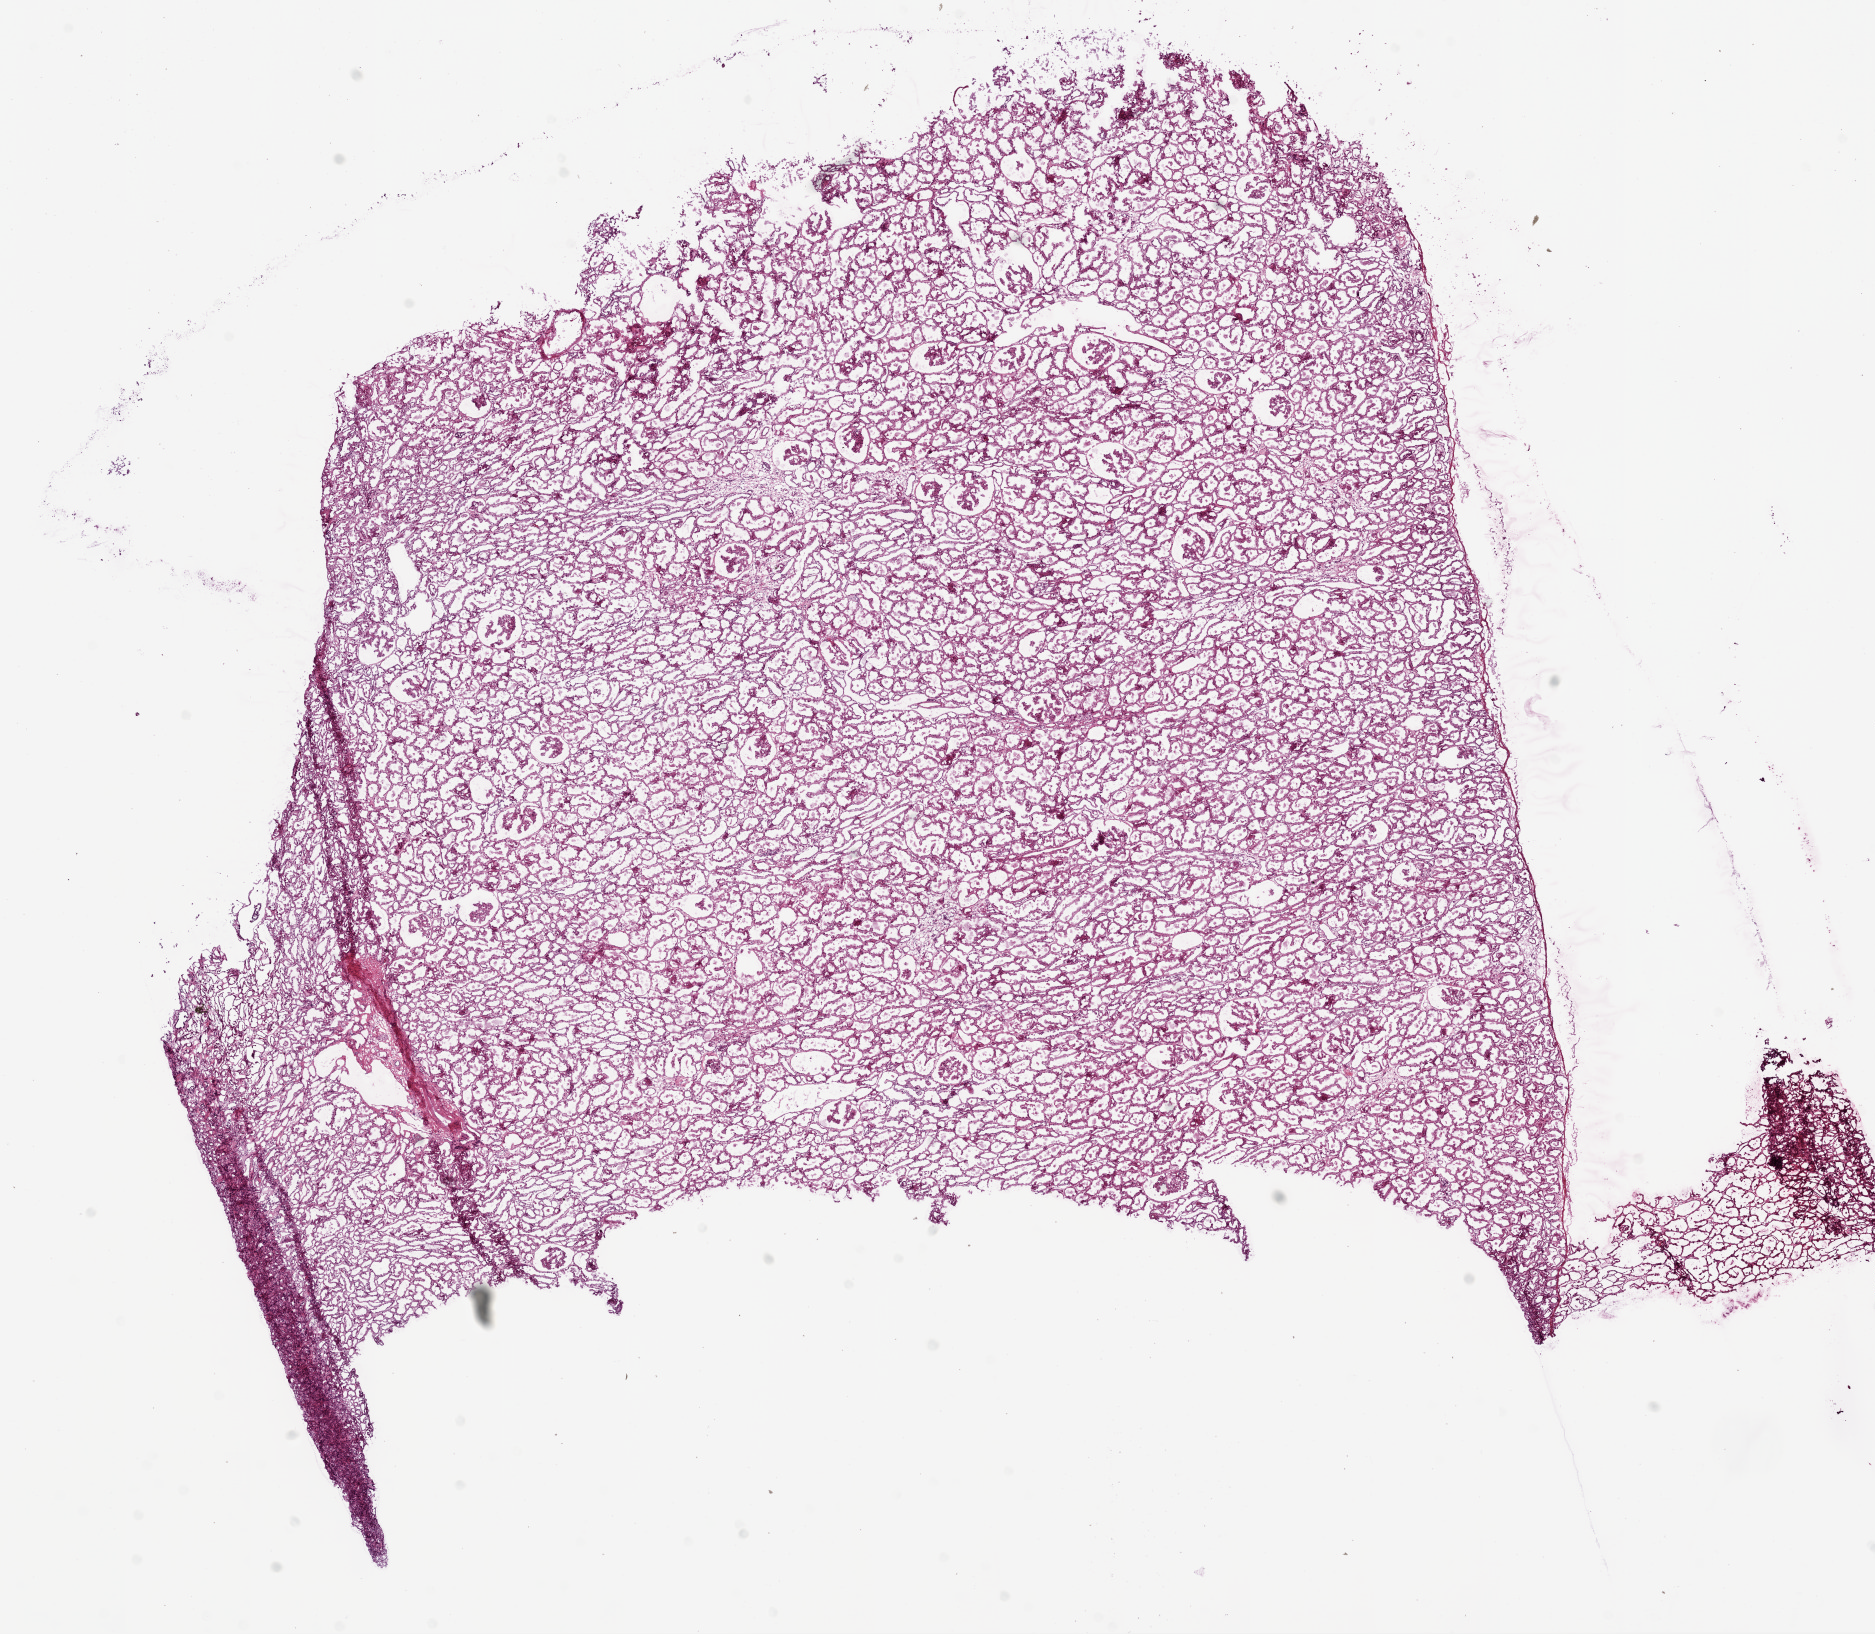
Hematoxylin and eosin (H&E) stained whole-slide image, whole scanned area (about 15.0 x 13.1 mm) shown as a low-resolution overview. Frozen section. Kidney, solid tissue normal (non-tumour tissue) sample. Male patient; age at initial diagnosis 49 years.
This section: solid tissue normal sample (biorepository sample class). Patient diagnosis: Clear cell adenocarcinoma, NOS.